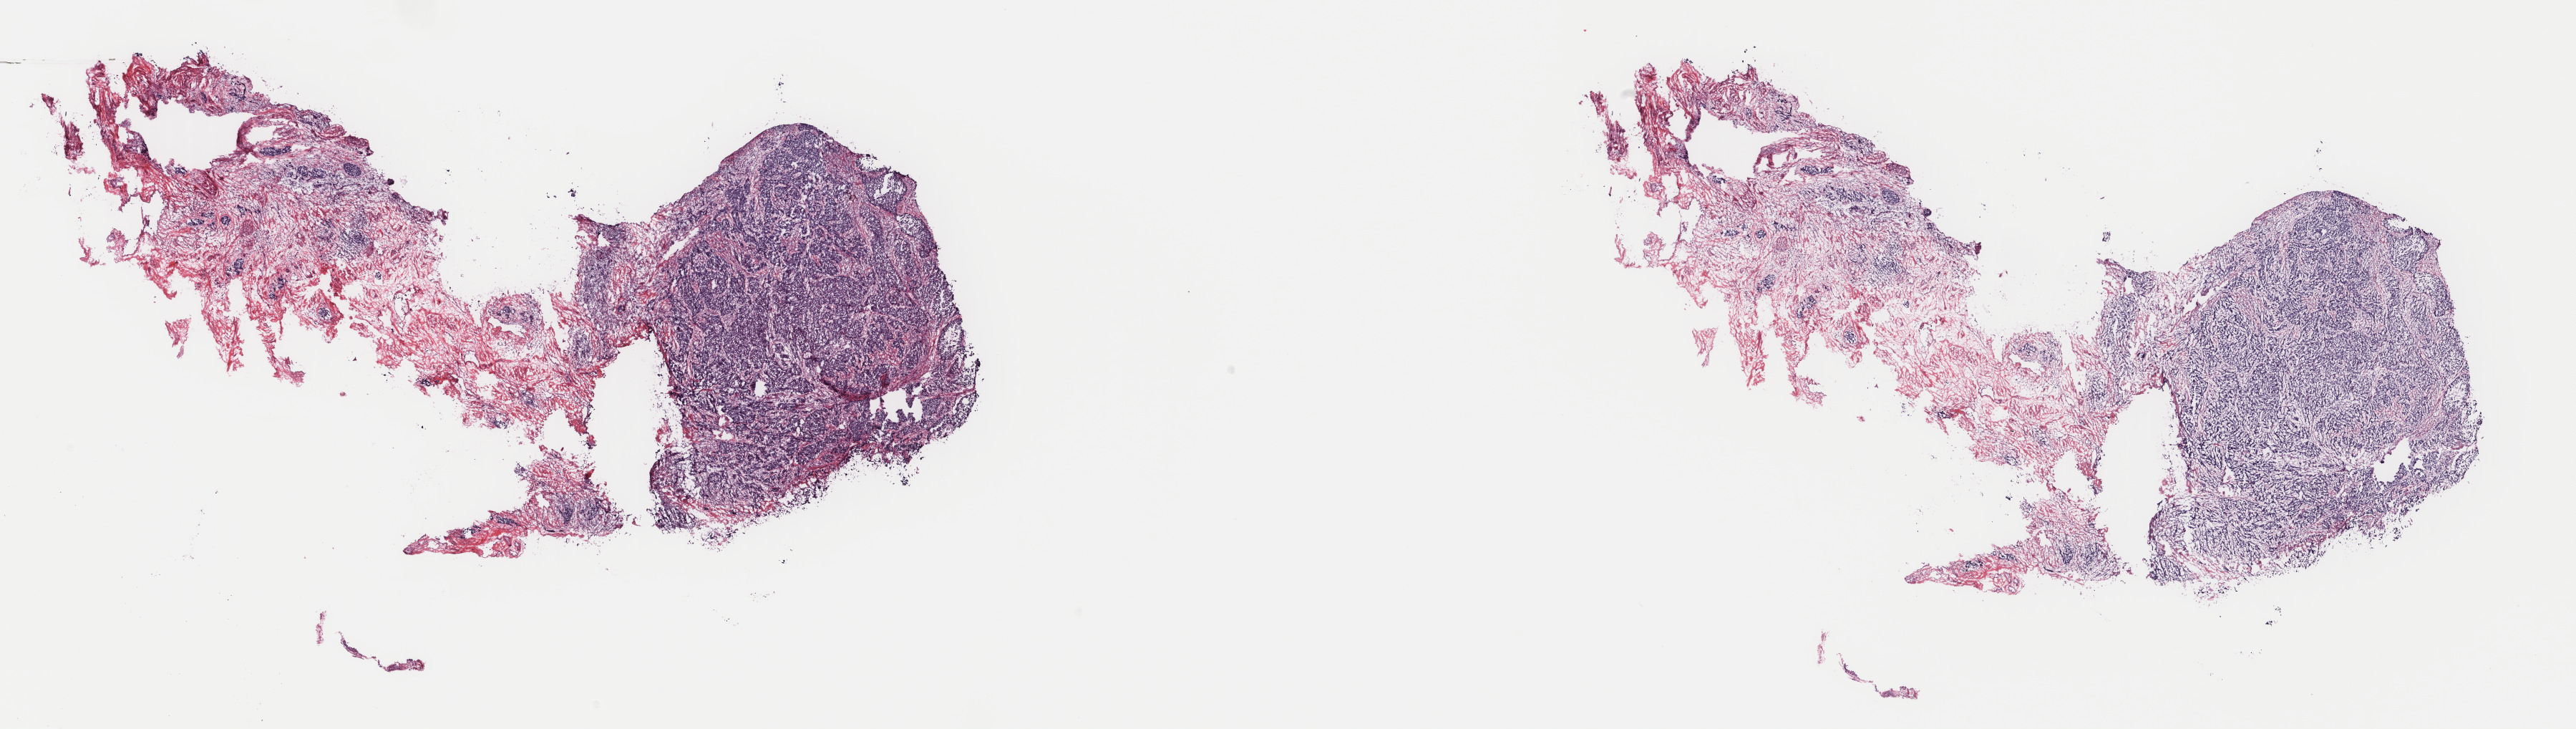
Digitized H&E tissue section (whole slide) — shown as a low-resolution overview of the whole scanned area (about 28.6 x 8.1 mm). Frozen section from the top of the tissue portion. Primary tumour sample from the cervix. Female patient; age at initial diagnosis 53 years. Histologic grade: G3 (poorly differentiated). Pathologist review of this section (percent, as recorded): tumour cells 65%, tumour nuclei 65%, normal cells 10%, stromal cells 20%, necrosis 5%. Inflammatory infiltration, as recorded: lymphocyte infiltration 4%, monocyte infiltration 1%, neutrophil infiltration 2%.
FIGO stage: II. Diagnosis: Adenocarcinoma, endocervical type (cervix uteri). Lymph nodes positive (case pathology): 0 of 2 examined.